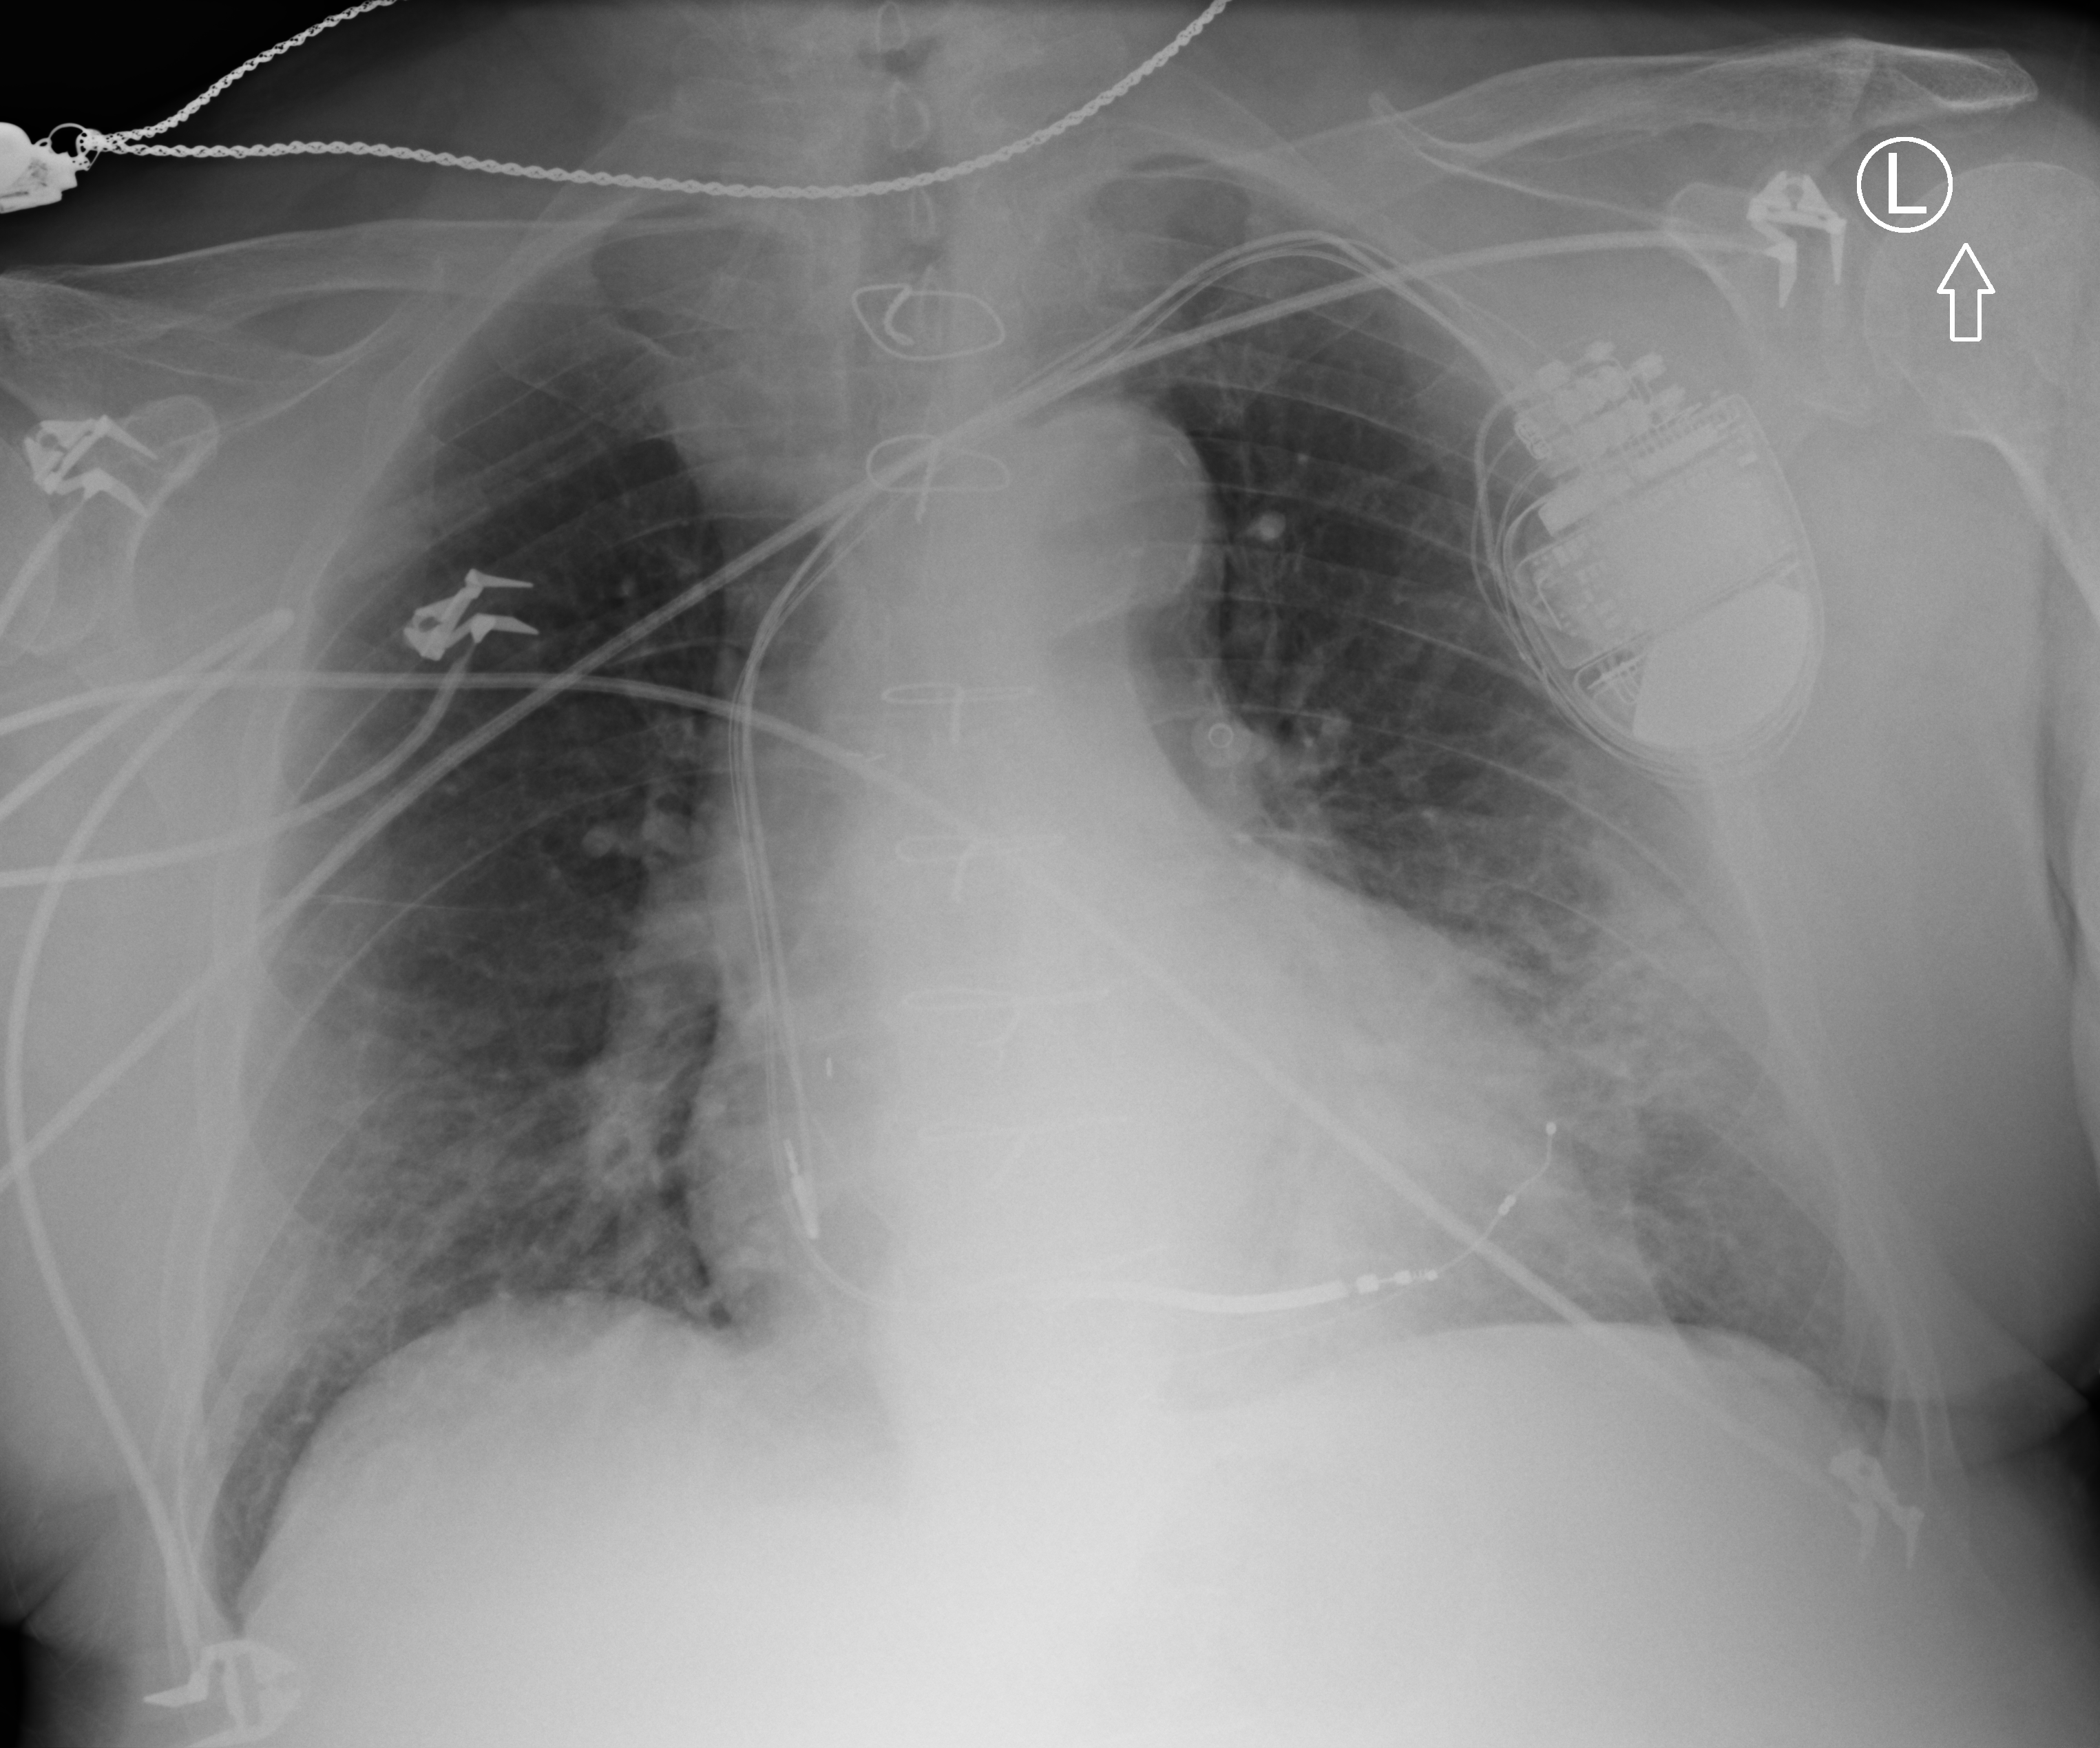
Bedside chest radiograph (computed radiography), anteroposterior (AP) projection. Male patient hospitalised with COVID-19, age 75–90 years.
From the hospital-stay record, not from the radiograph (when in the stay this image was taken is not recorded):
- admitted to intensive care during this hospital stay: no
- mechanically ventilated during this hospital stay: no